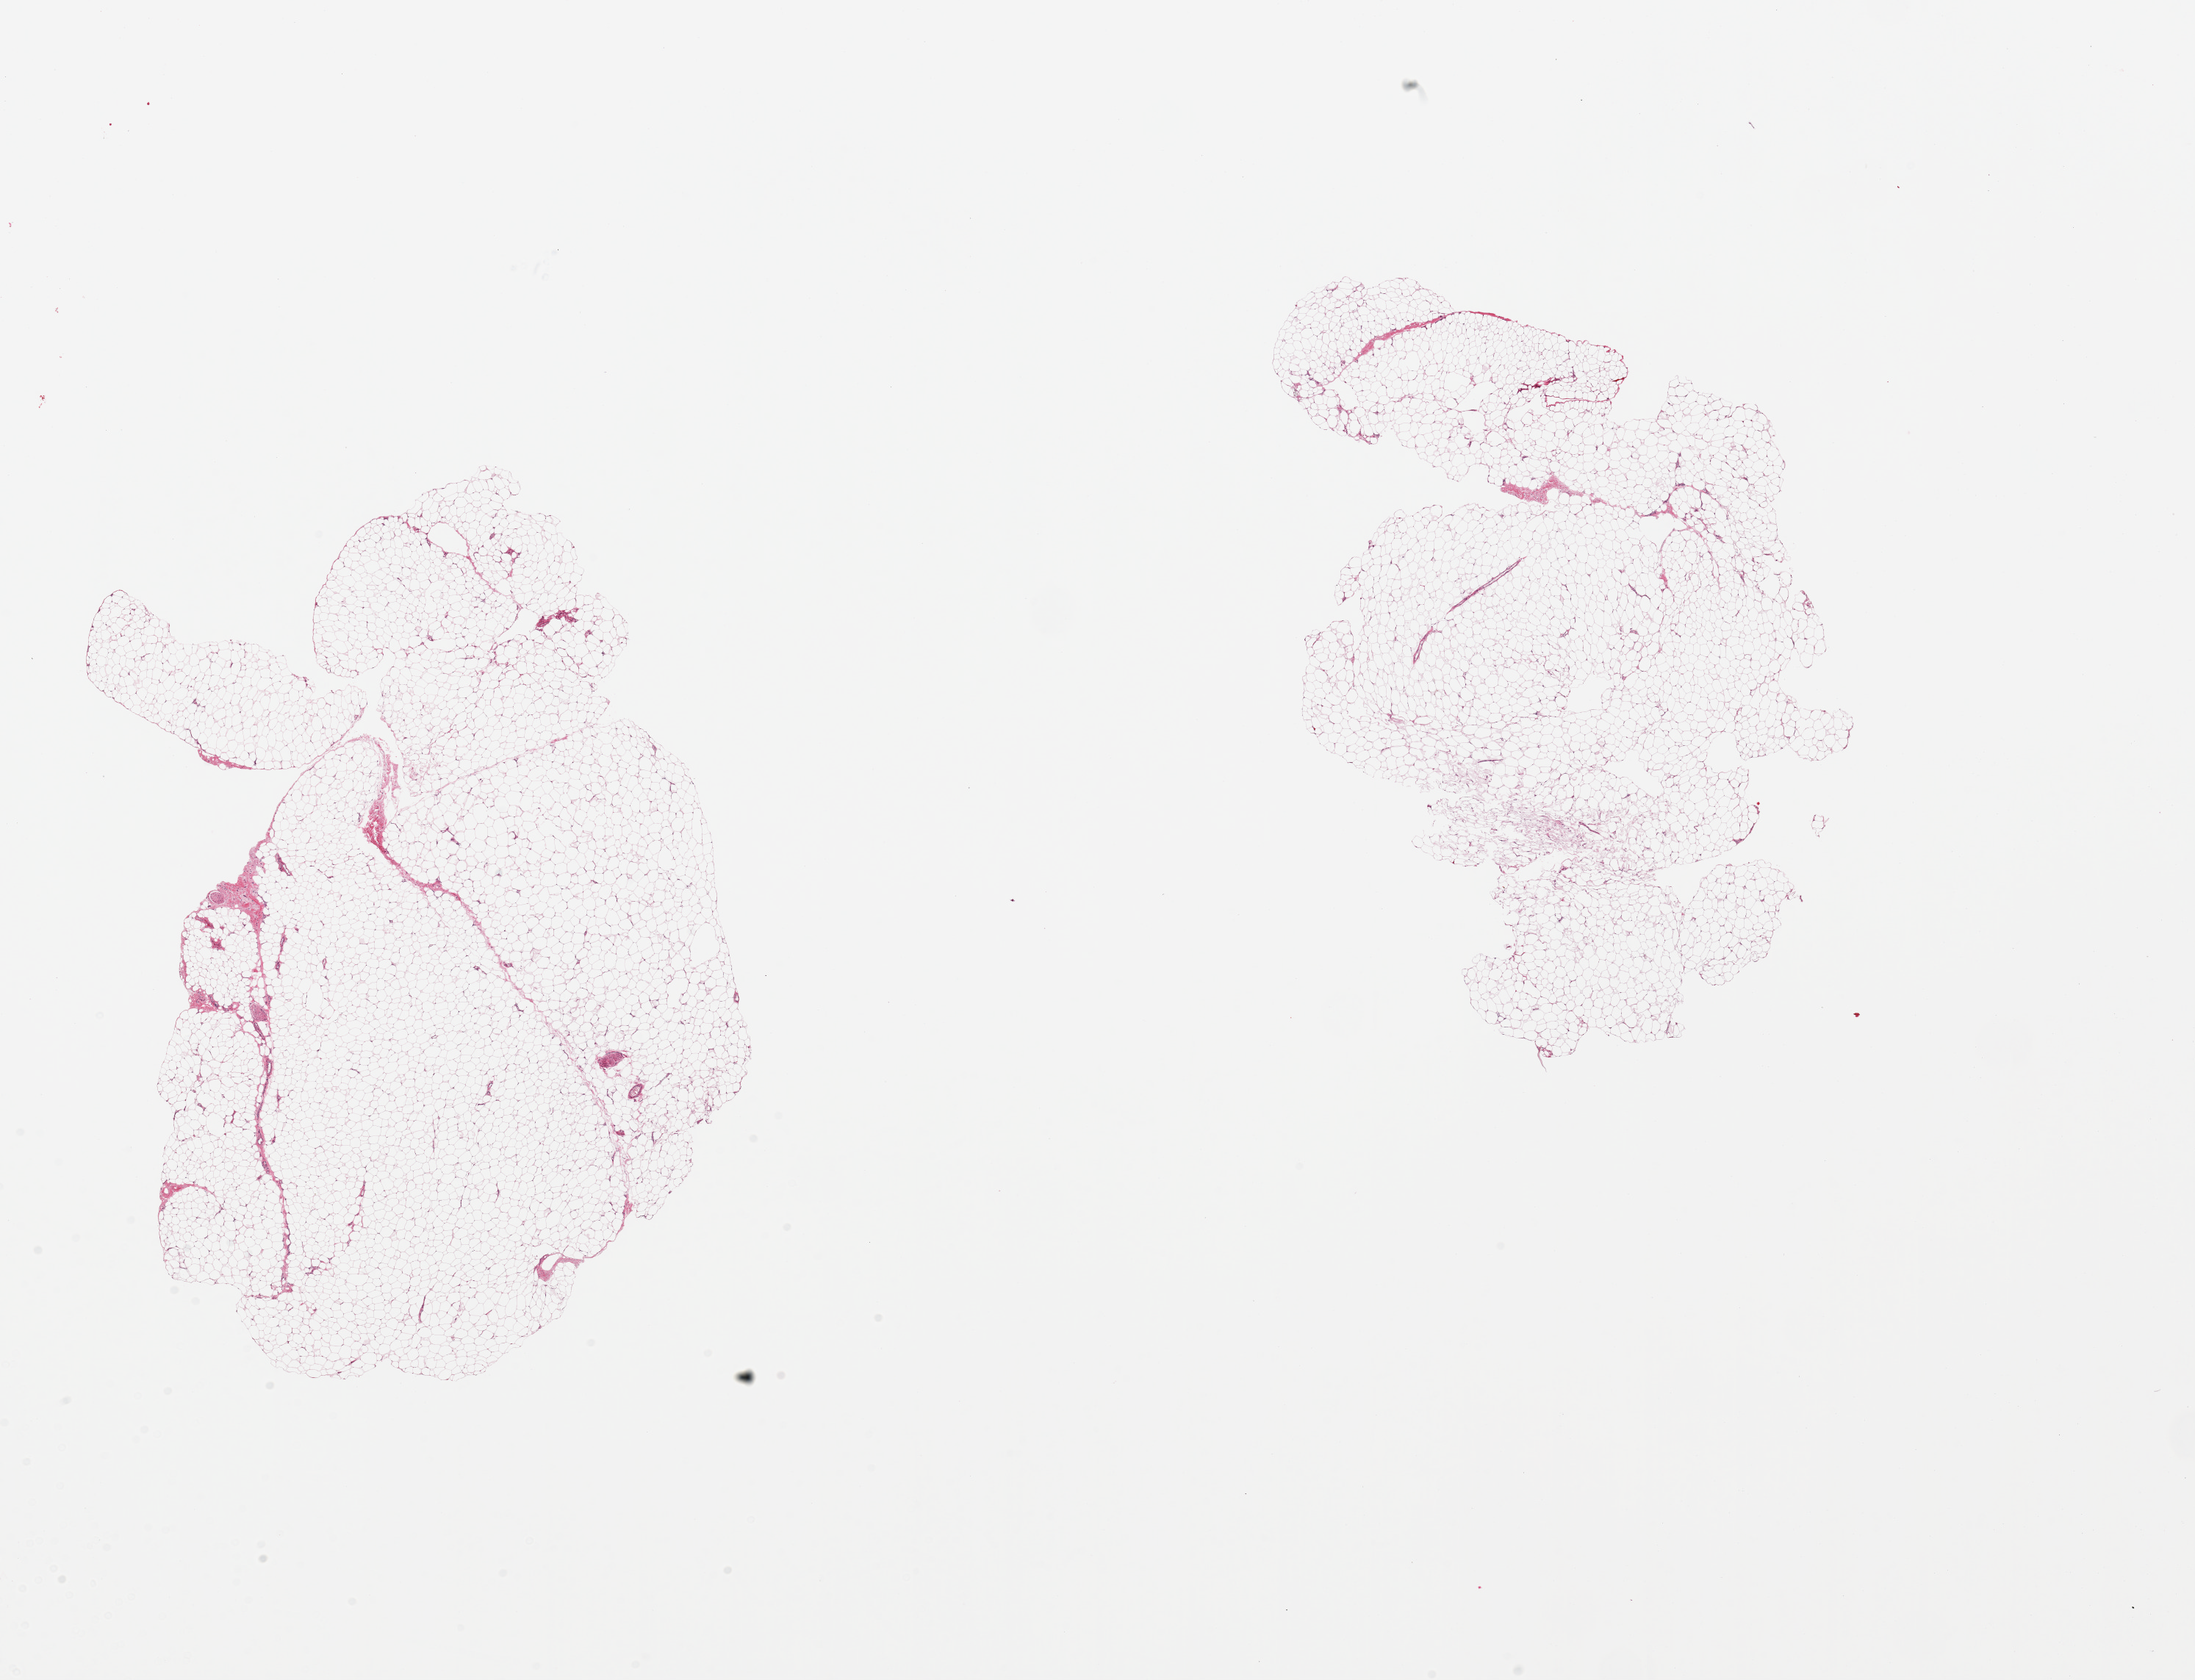
Haematoxylin and eosin whole-slide image, brightfield — shown as a low-resolution overview of the whole scanned area (about 23.6 x 18.1 mm, acquisition: 20x scan). PAXgene-fixed paraffin-embedded (PFPE) section. Target tissue: adipose tissue. Tissue donor sample. Donor: female.
Review note (as recorded): 2 pieces; minimal fibrous content.